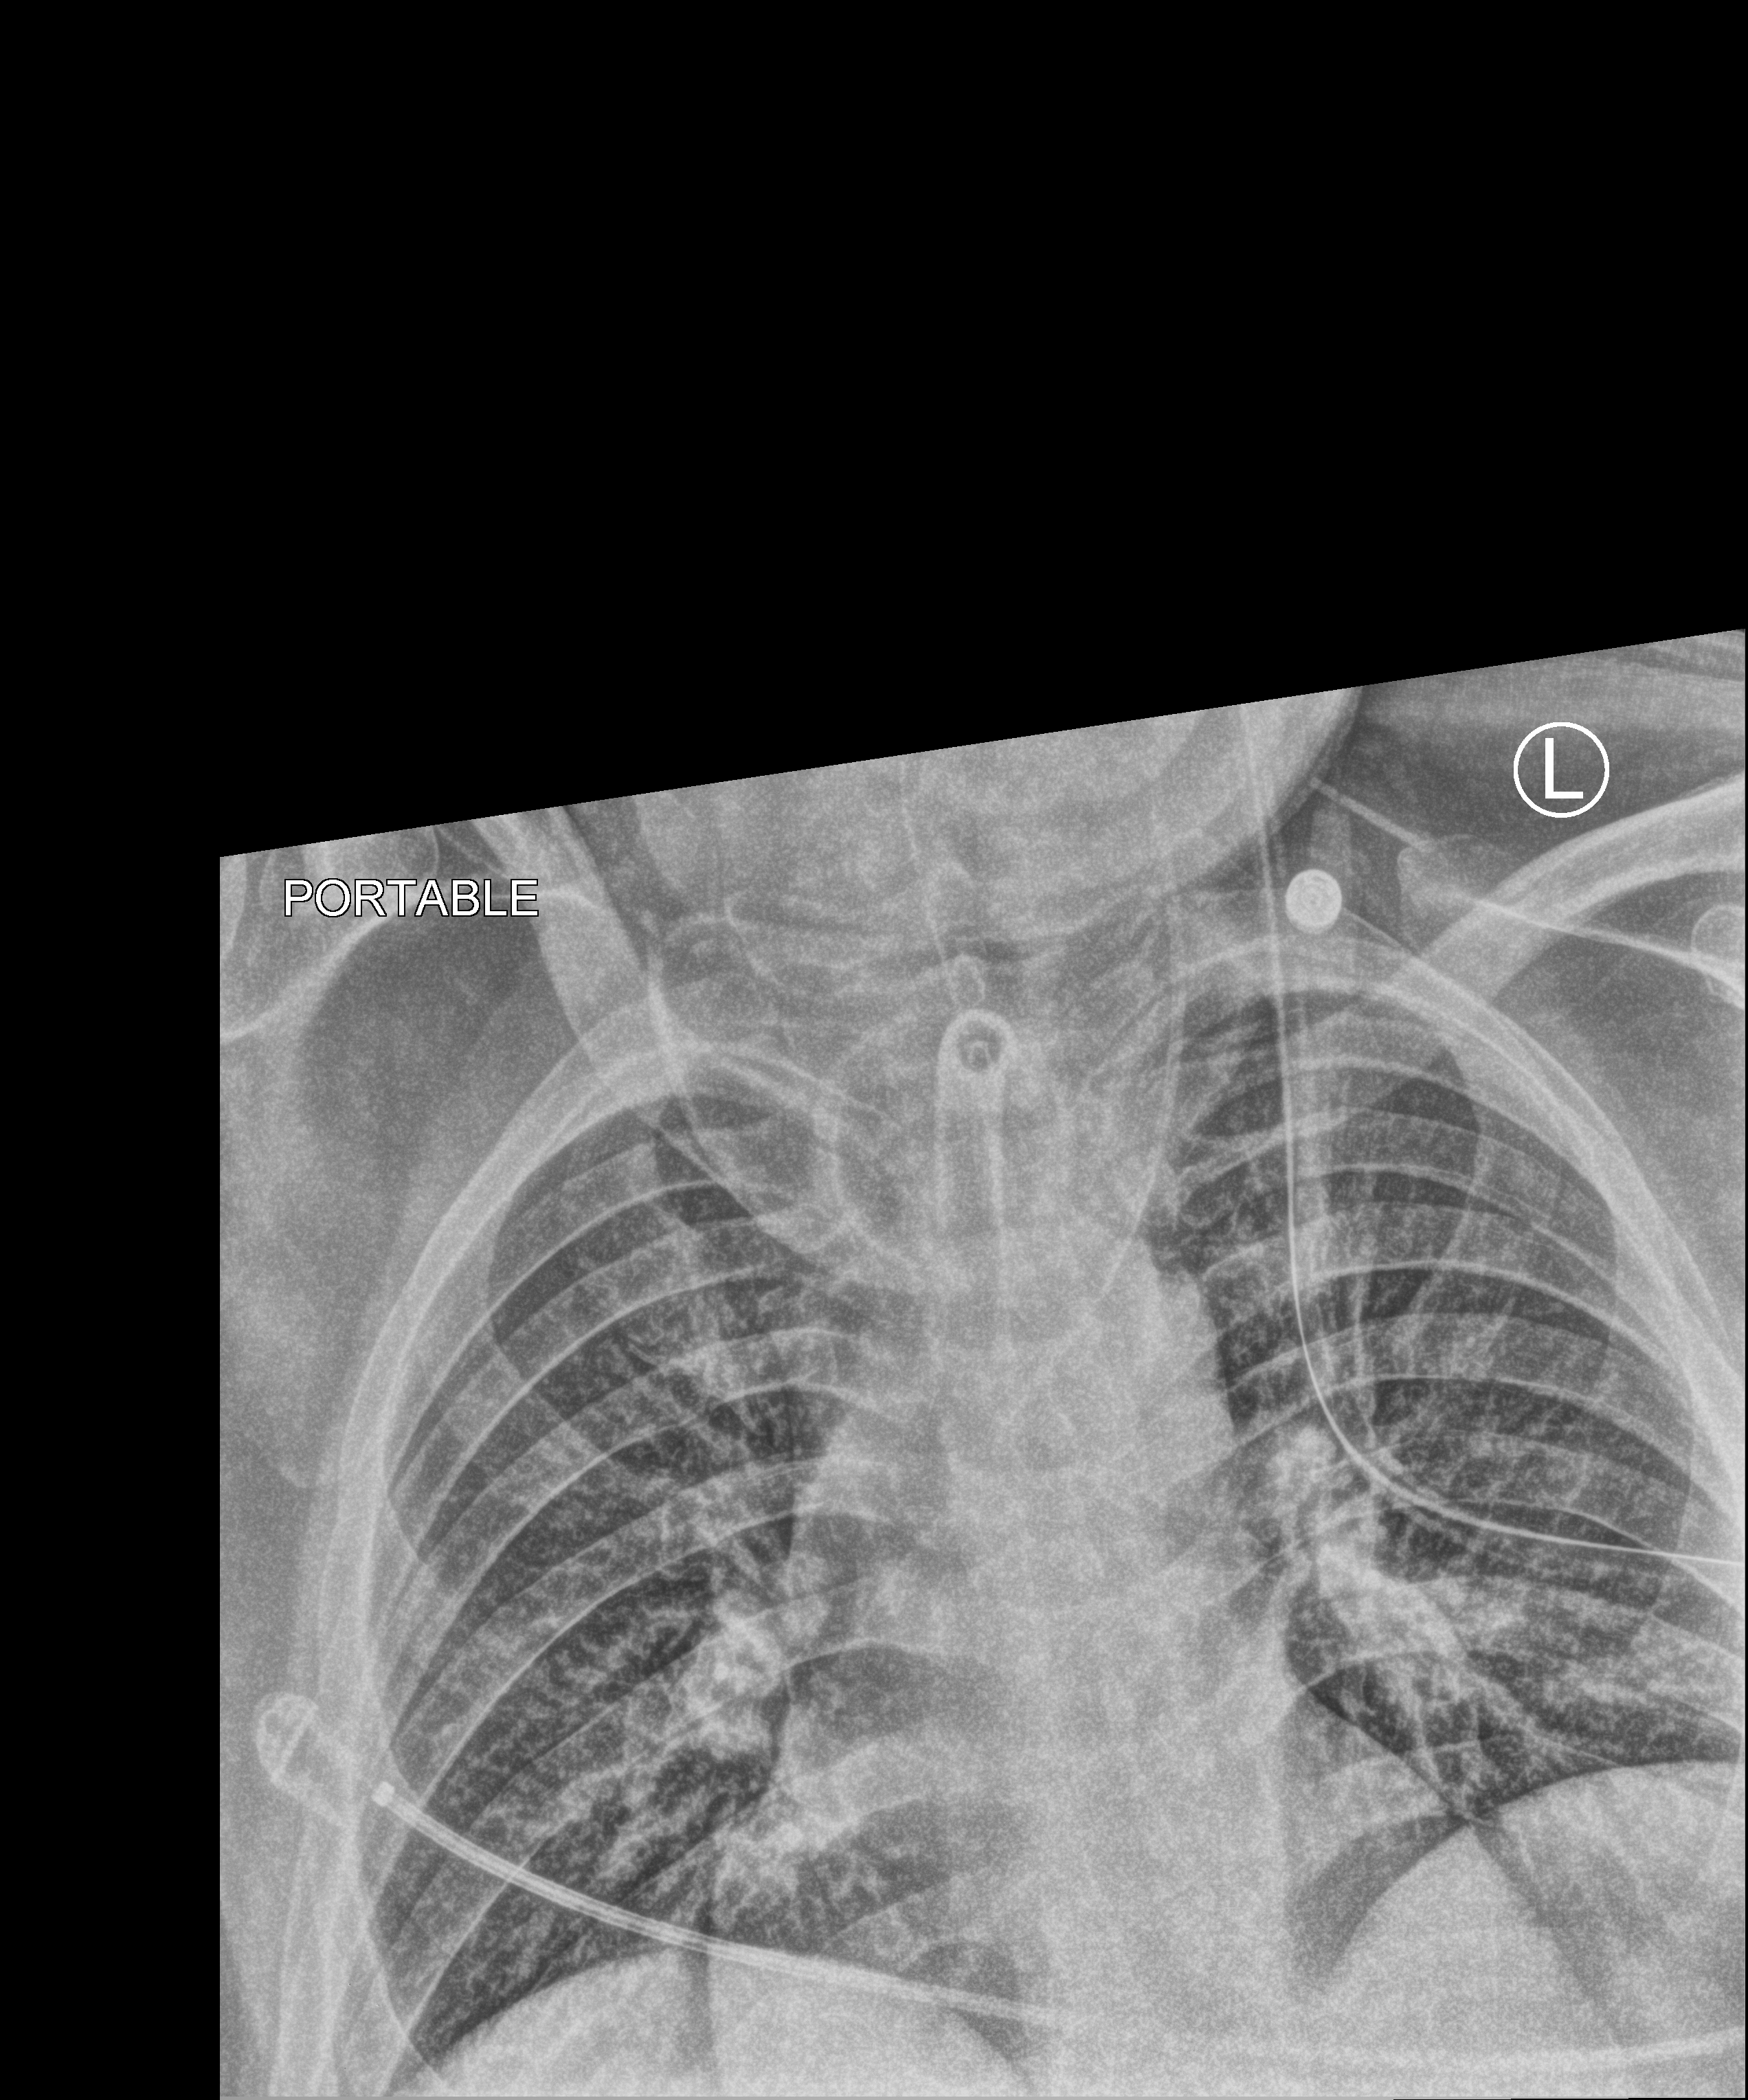
Bedside chest radiograph (computed radiography); anteroposterior (AP) projection. Patient hospitalised with COVID-19; male, aged 18–59 years.
Admission-level facts for this patient (not findings on this image; timing relative to this image not recorded): admitted to intensive care during this hospital stay: yes; mechanically ventilated during this hospital stay: yes; length of hospital stay: 65 days.